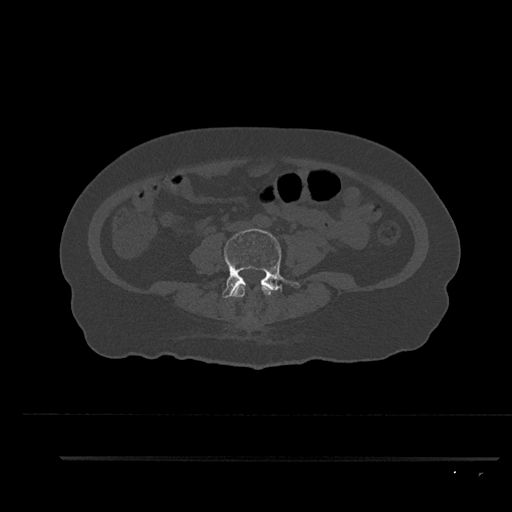
CT including the spine, one axial slice. Position 38 of 797 along the scan axis. Reconstruction kernel Br40s/3. 120 kVp. Bone window (W 1800 / L 400 HU). 0.5 mm slice thickness. 512 × 512 image matrix. Female patient, age 44 years. From the clinical record (not read from this slice): primary cancer: renal; vertebrae with lytic lesions (as recorded): L1.
Annotated regions visible in this slice (semi-automatically segmented with operator editing):
- L3 vertebra: bounding box [x1, y1, x2, y2] px = [232, 284, 272, 297]
- L4 vertebra: [222, 228, 300, 298]